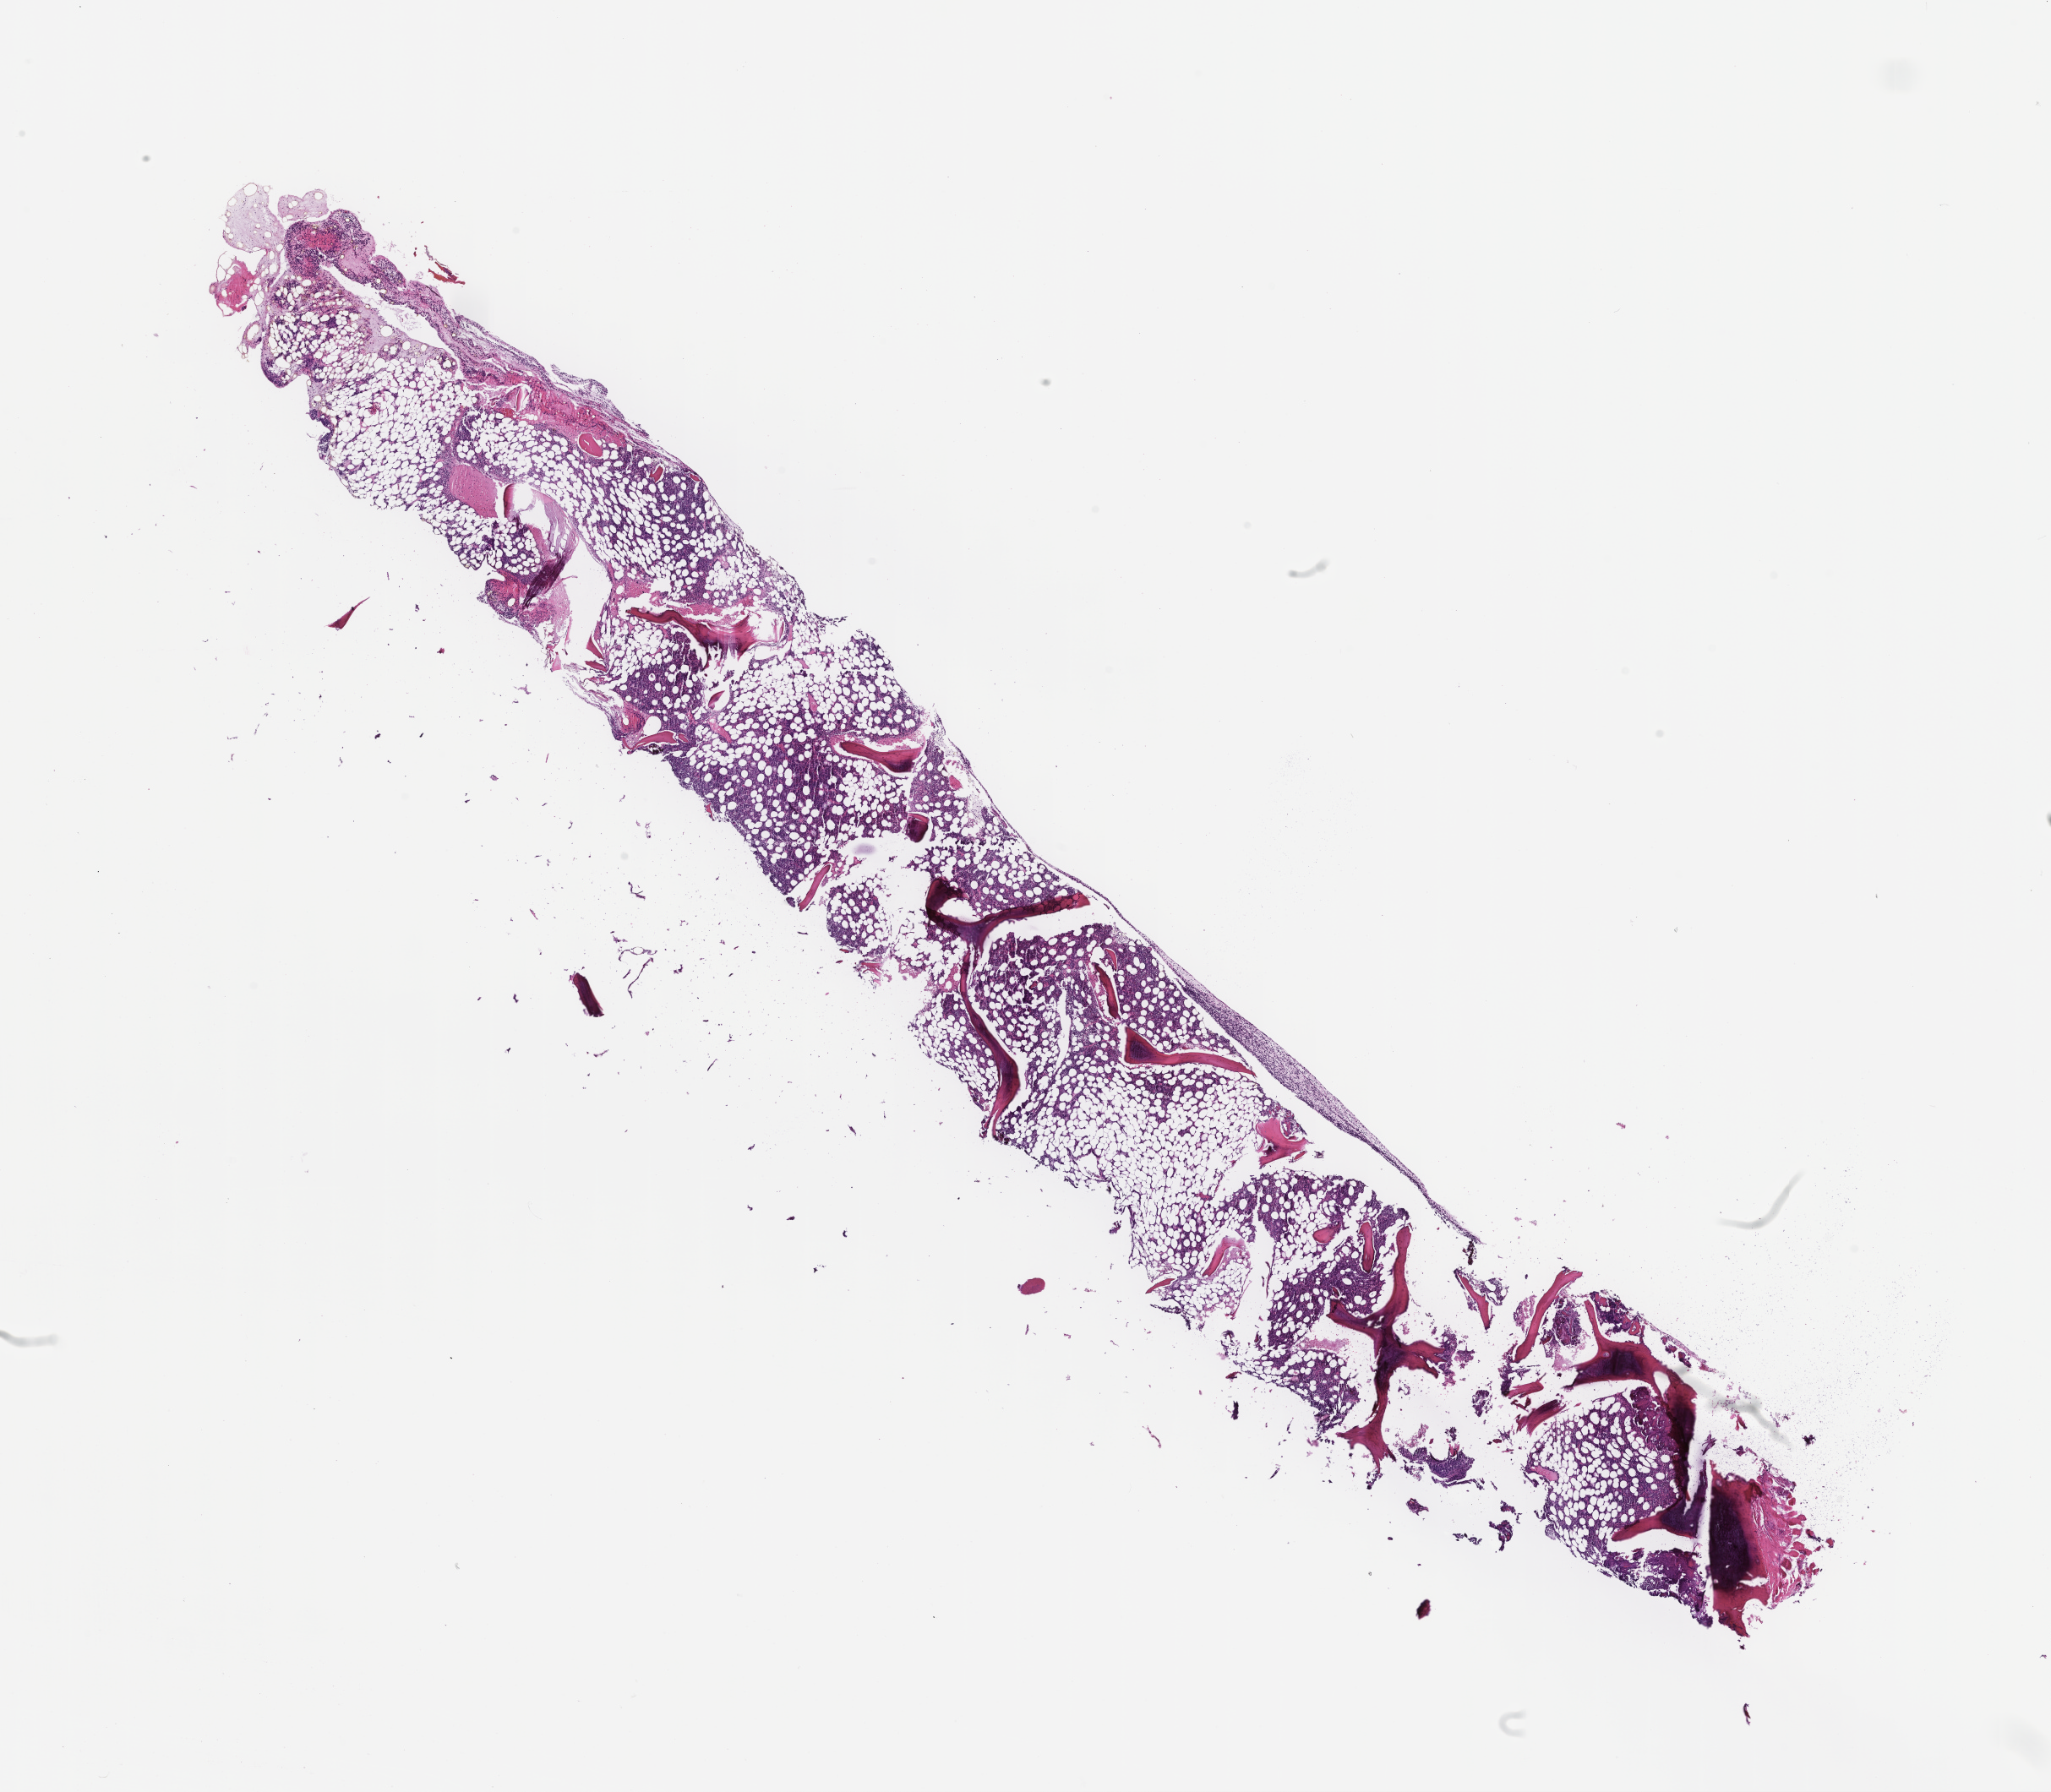
H&E whole-slide image — low-resolution overview of the scanned area, about 19.6 x 17.1 mm. Formalin-fixed paraffin-embedded section. Site: bone marrow. Specimen time point: archival tissue. Patient: male.
This section: primary tumour tissue. Diagnosis: Plasma Cell Myeloma.